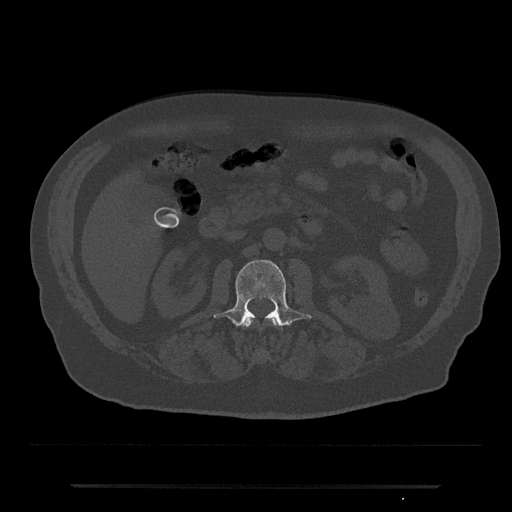
CT including the spine, one axial slice. Position 483 of 797 along the scan axis. Reconstruction kernel Br40s/3. 120 kVp. Bone window (W 1800 / L 400 HU). 0.5 mm slice thickness. 512 × 512 image matrix, field of view 434 × 434 mm. Male patient, age 80 years. Case-level facts recorded for this patient, not image findings: primary cancer: prostate; vertebrae with lytic lesions (as recorded): L1, T11.
Annotated regions visible in this slice (semi-automatic segmentation, software-assisted and operator-edited):
- L1 vertebra: bounding box (x1, y1, x2, y2) in pixels: (243, 318, 279, 327)
- L2 vertebra: (214, 260, 312, 326)